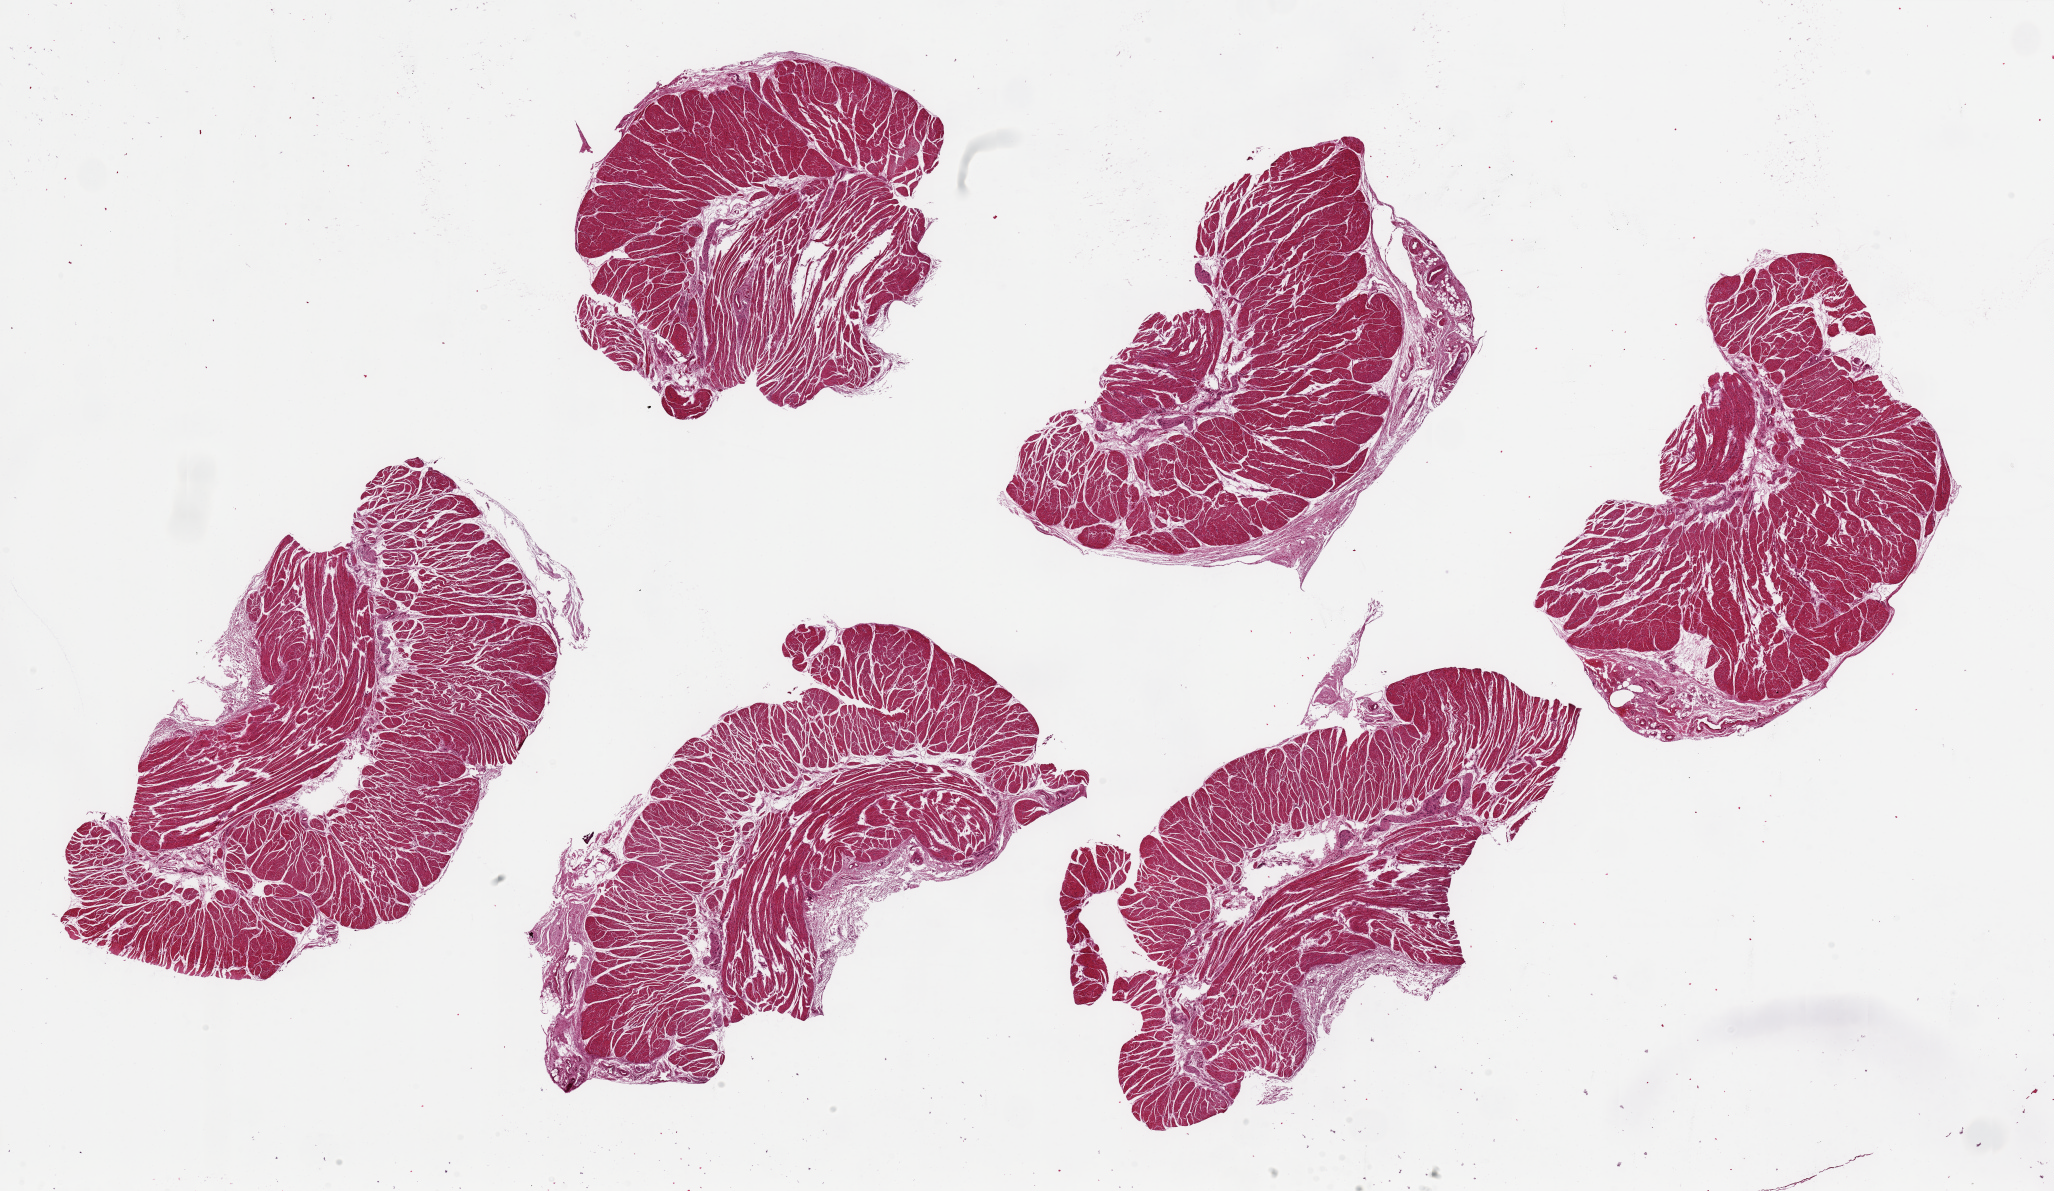
Digitized H&E-stained section — shown as a low-resolution overview of the whole scanned area (about 32.5 x 18.8 mm, acquisition: 20x scan). PAXgene-fixed, paraffin-embedded tissue. Sampled site (target tissue): esophageal muscle. Donor tissue sample. Donor sex: female.
Review note (as recorded): 6 pieces up to 9x4 mm.